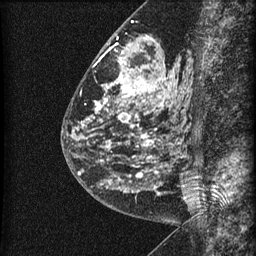
Breast MRI (dynamic contrast-enhanced), one sagittal slice; slice 25 of 60 in the series (ordered by position); dynamic contrast-enhanced series, image 2 of 3 at this slice position (ordered by acquisition); 1.5 T; TE 4.2 ms, TR 22.7 ms; 1.5 mm slice thickness; 256 × 256 image matrix, field of view 180 × 180 mm. Patient: female, 48 years. Case-level facts recorded for this patient, not image findings: setting: breast cancer imaged before/during neoadjuvant chemotherapy; receptor status: triple-negative.
Structures marked on this image (semi-automatic segmentation, software-assisted and operator-edited):
- analysis volume of interest (the breast-tissue region the enhancement analysis was run in; not a lesion): bounding box [x1, y1, x2, y2] px = [81, 23, 186, 202]
- tumour enhancement mask (voxels above the 90 % enhancement threshold inside the analysis volume of interest): [82, 37, 174, 192]